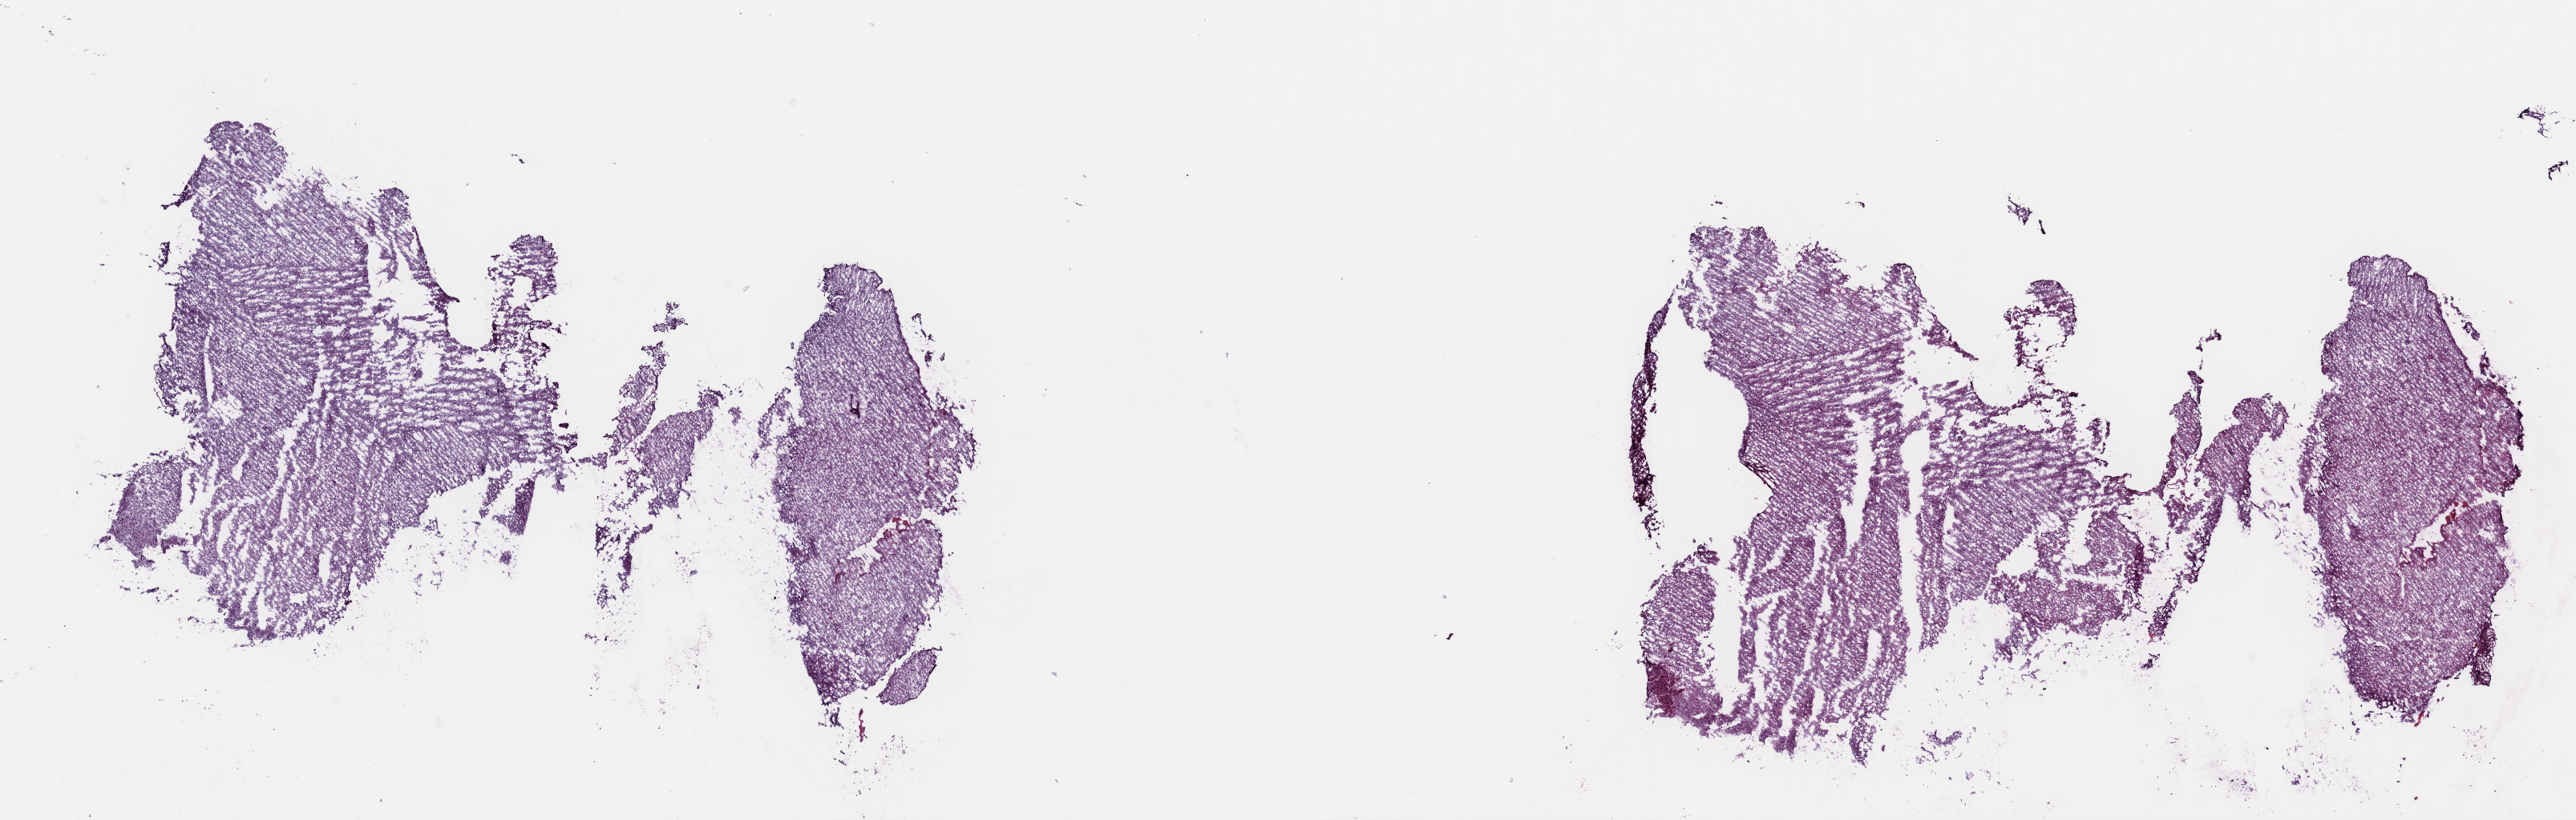
Digitized Hematoxylin and eosin (H&E) stained tissue section (whole slide) — low-resolution overview of the scanned area, about 25.4 x 8.1 mm (slide scanned at 40x). Frozen section from the top of the tissue portion. Sample: recurrent tumour, brain. Female patient; age at initial diagnosis 34 years. Composition of this section per pathologist review: tumour cells 45%, tumour nuclei 90%, normal cells 10%, stromal cells 45%, necrosis 0%. Infiltration values recorded for this section: lymphocyte infiltration 0%, monocyte infiltration 0%, neutrophil infiltration 0%.
- this section: recurrent tumour
- patient diagnosis: Oligodendroglioma, NOS